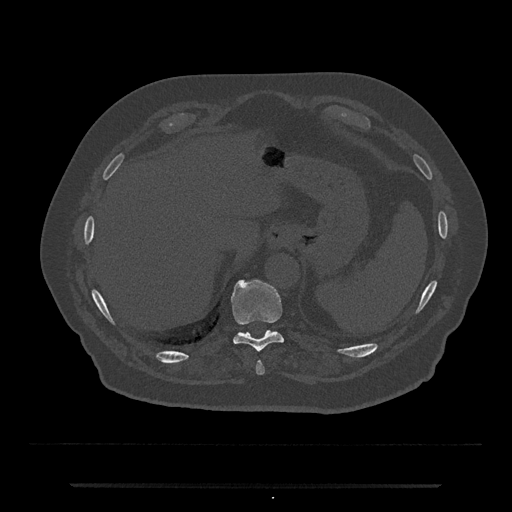
CT including the spine, one axial slice; reconstruction kernel Br40s/3; 120 kVp; bone window (W 1800 / L 400 HU); 0.5 mm slice thickness; 512 × 512 image matrix, field of view 434 × 434 mm. Patient: male, 80 years. Case-level facts recorded for this patient, not image findings: primary cancer: prostate; vertebrae with lytic lesions (as recorded): L1, T11.
Structures marked on this image (semi-automatic segmentation, software-assisted and operator-edited):
- T10 vertebra: bounding box [x1, y1, x2, y2] px = [230, 279, 284, 352]
- T9 vertebra: [256, 361, 265, 375]